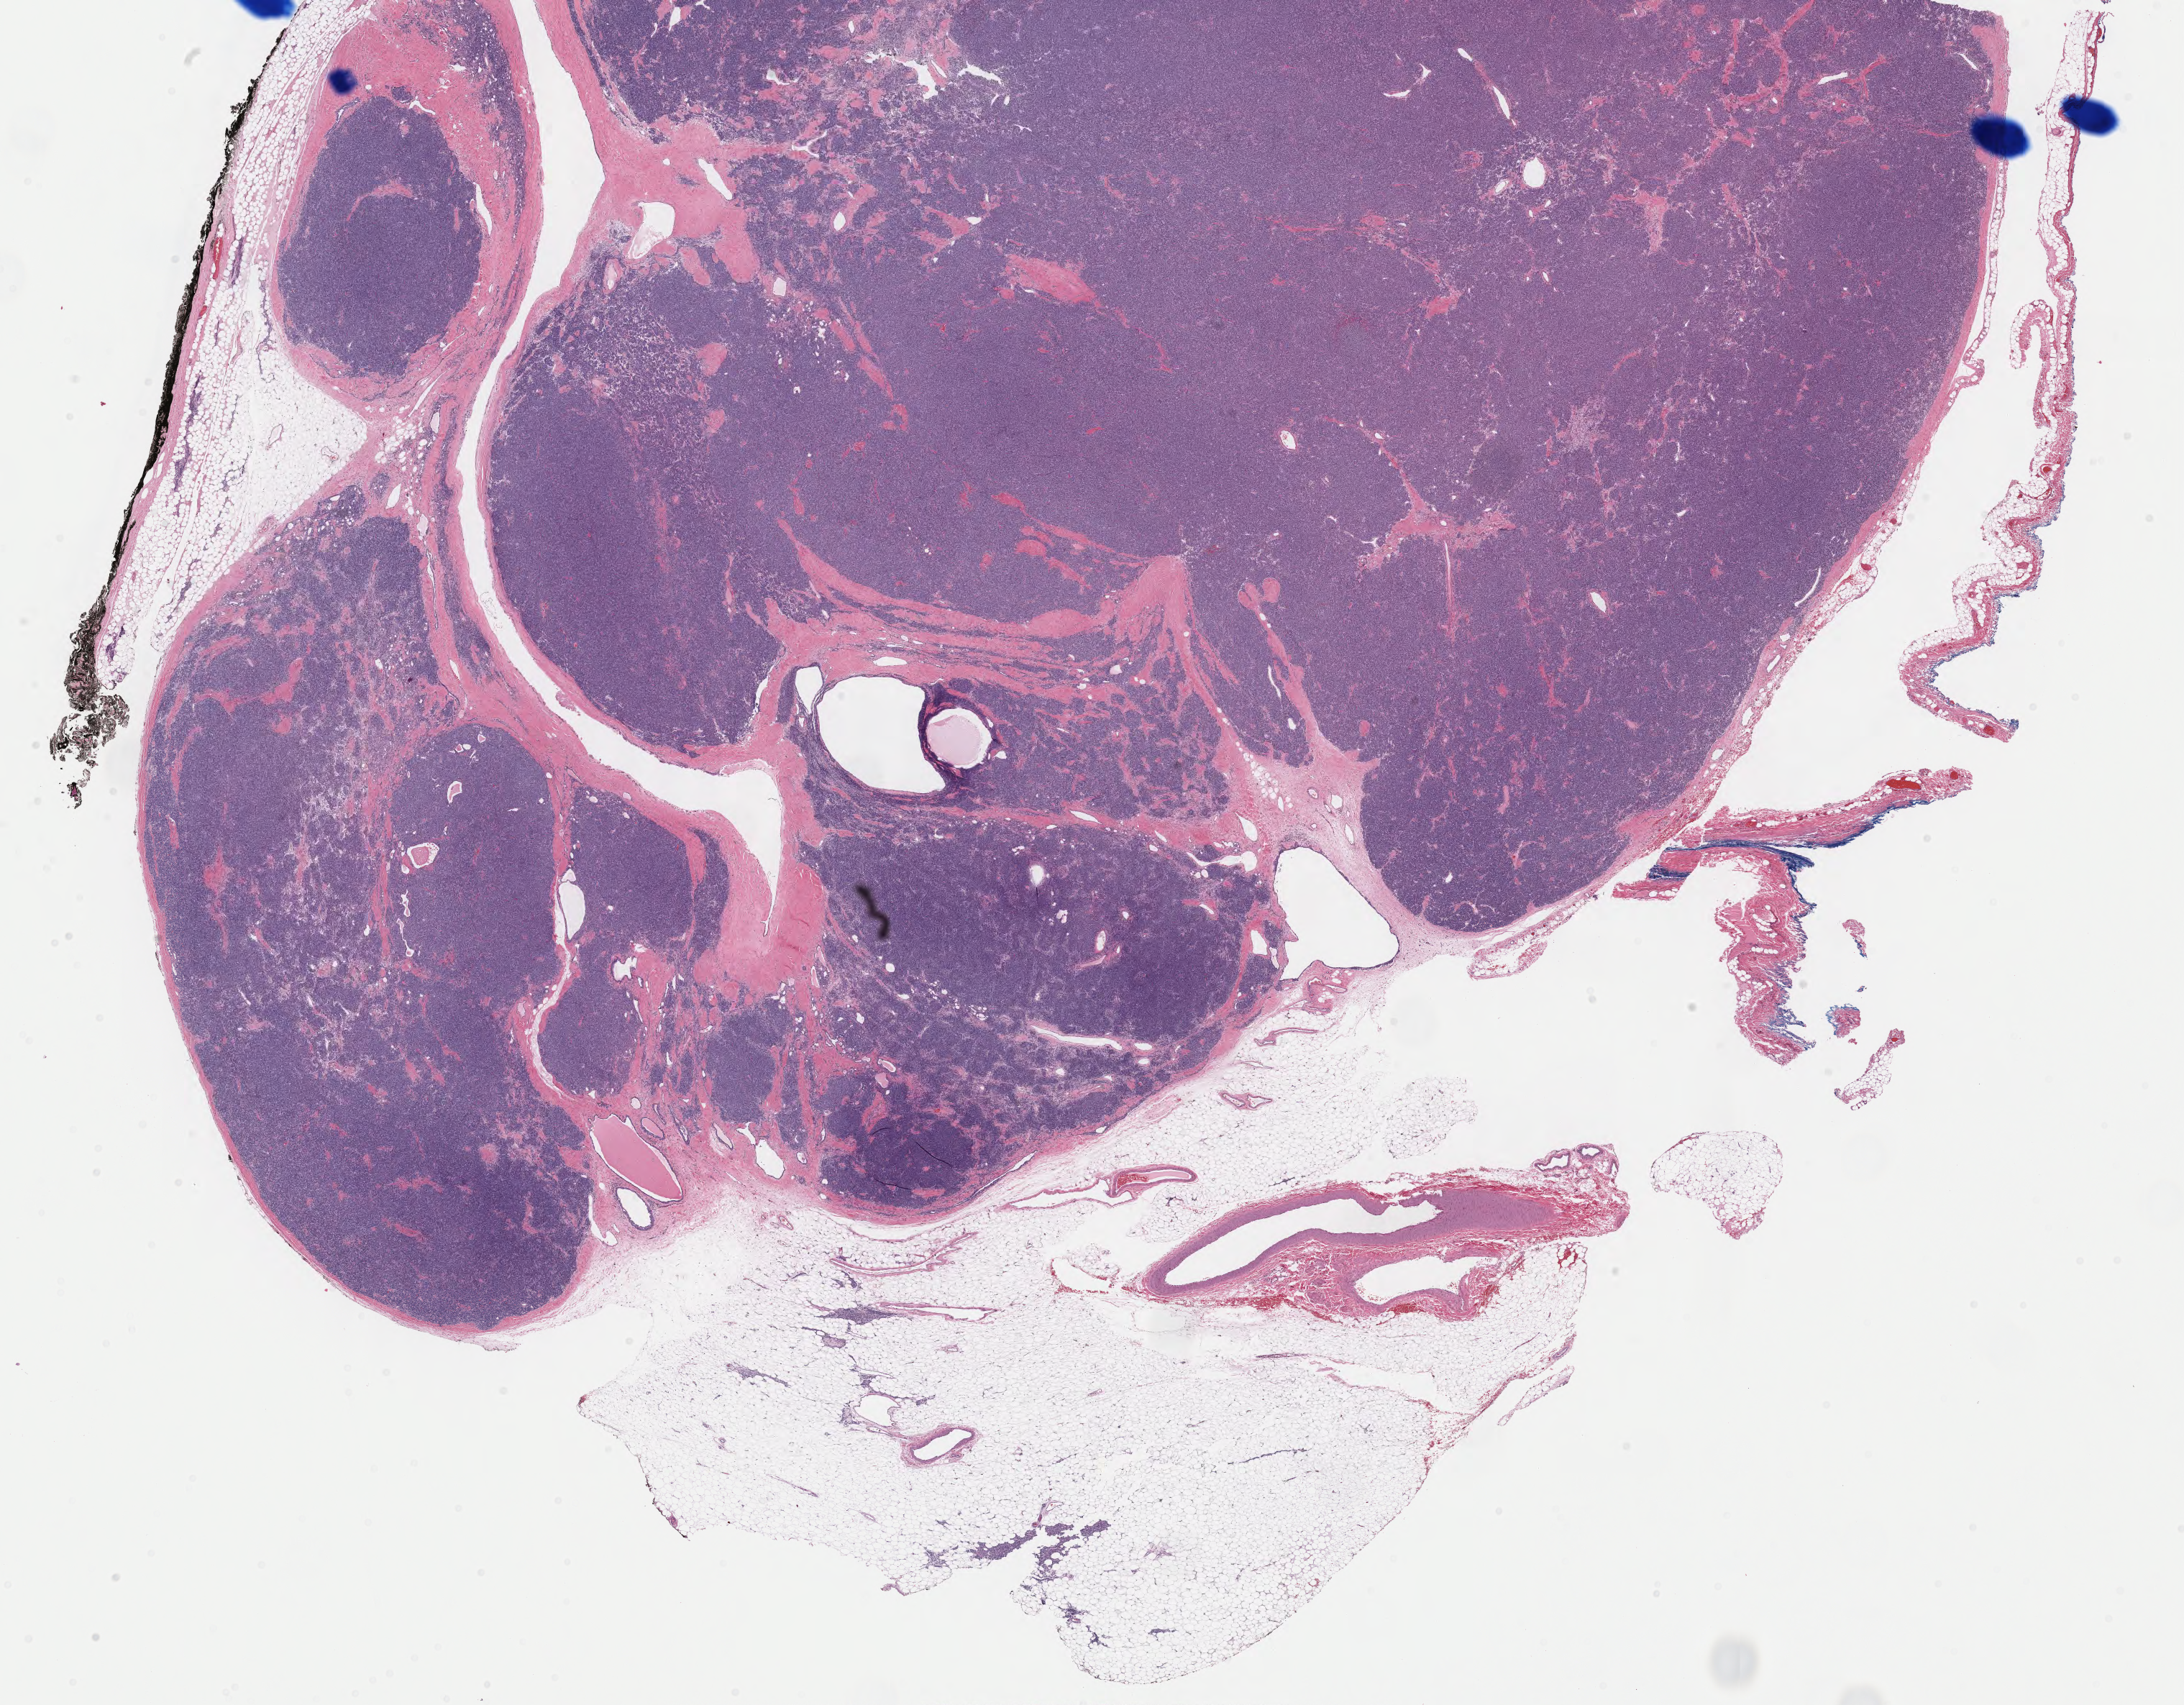
Digitized Hematoxylin and eosin (H&E) stained tissue section (whole slide) — low-resolution overview of the scanned area, about 24.1 x 18.8 mm (from a 40x scan); formalin-fixed paraffin-embedded (FFPE) diagnostic section; primary tumour sample from the thymus. Male patient; age at initial diagnosis 52 years.
- histologic diagnosis: Thymoma, type A, malignant